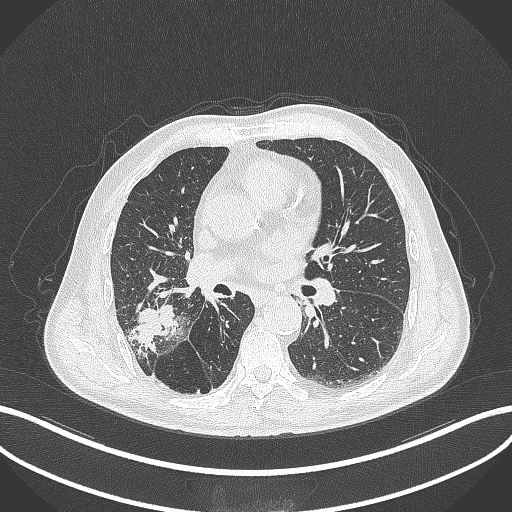
Chest CT, one axial slice; position 219 of 429 along the scan axis; reconstruction kernel B70f; 120 kVp; lung window (W 1500 / L -600 HU); 1 mm slice thickness; 512 × 512 image matrix, field of view 400 × 400 mm. Male patient, age 72 years. From the clinical record (not read from this slice): clinical TNM (as recorded): T3 N2 M0.
Outlined on this slice (rectangle marked by the reading radiologist):
- lung tumour (recorded histology: adenocarcinoma): bounding box (x1, y1, x2, y2) in pixels: (123, 303, 181, 354)